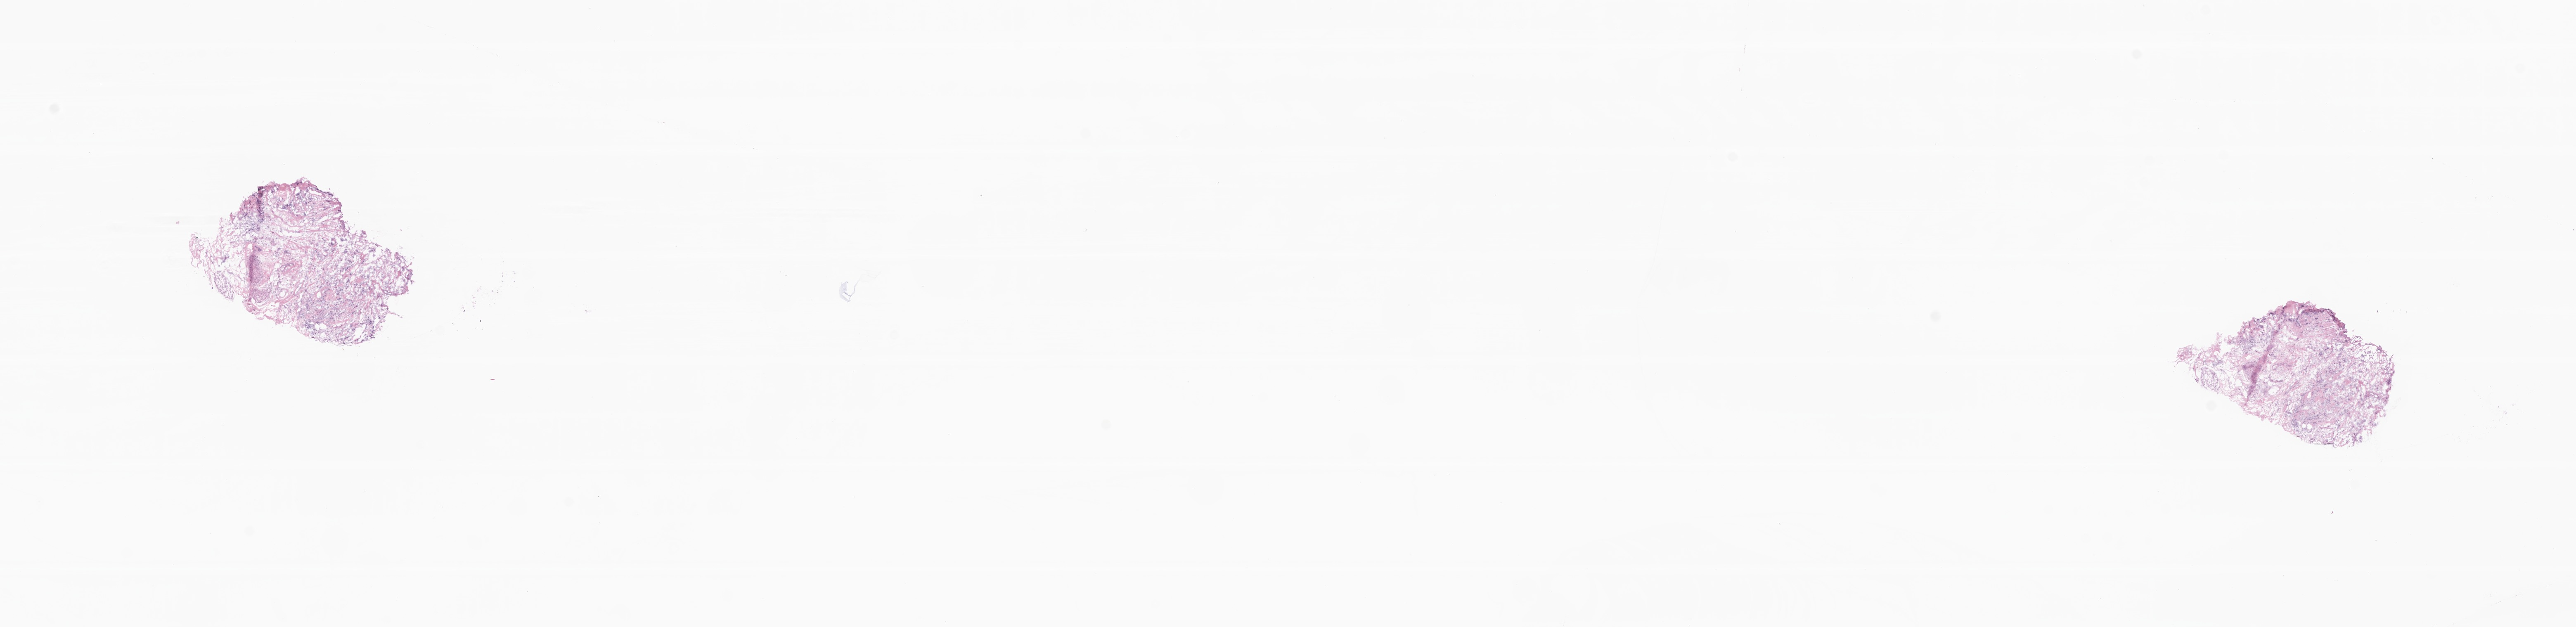
Digitized haematoxylin and eosin-stained section — shown as a low-resolution overview of the whole scanned area (about 26.3 x 6.4 mm); frozen section (tissue freezing medium); specimen: primary tumor; site: breast (right). Patient: female, age at initial diagnosis 79 years. Composition of this section per pathologist review: tumor cells 95%, tumor nuclei 80%, stromal cells 0%, necrosis 0%, normal cells 5%. Infiltration values recorded for this section: lymphocyte infiltration 0%, monocyte infiltration 0%, neutrophil infiltration 0%.
Diagnosis: Infiltrating duct carcinoma, NOS. Section: top of the tissue portion.